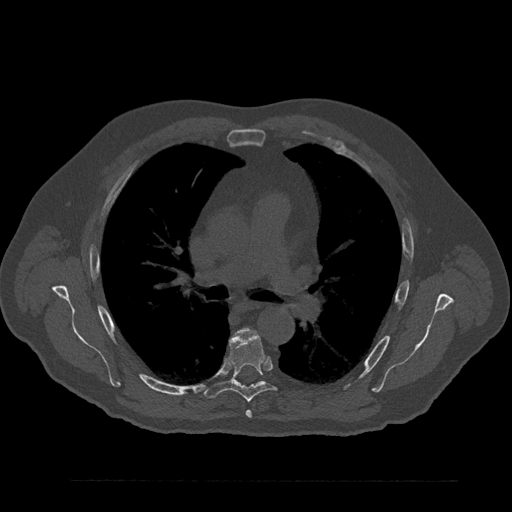
CT including the spine, one axial slice; slice 561 of 797 in the series (ordered by position); reconstruction kernel Br40s/3; bone window (W 1800 / L 400 HU); 0.5 mm slice thickness; 512 × 512 image matrix. Patient: male, 61 years. From the clinical record (not read from this slice): primary cancer: prostate.
Annotated regions visible in this slice (semi-automatic segmentation, software-assisted and operator-edited):
- T5 vertebra: bounding box <246,410,252,418> (left, top, right, bottom; pixels)
- T6 vertebra: <204,332,276,402>